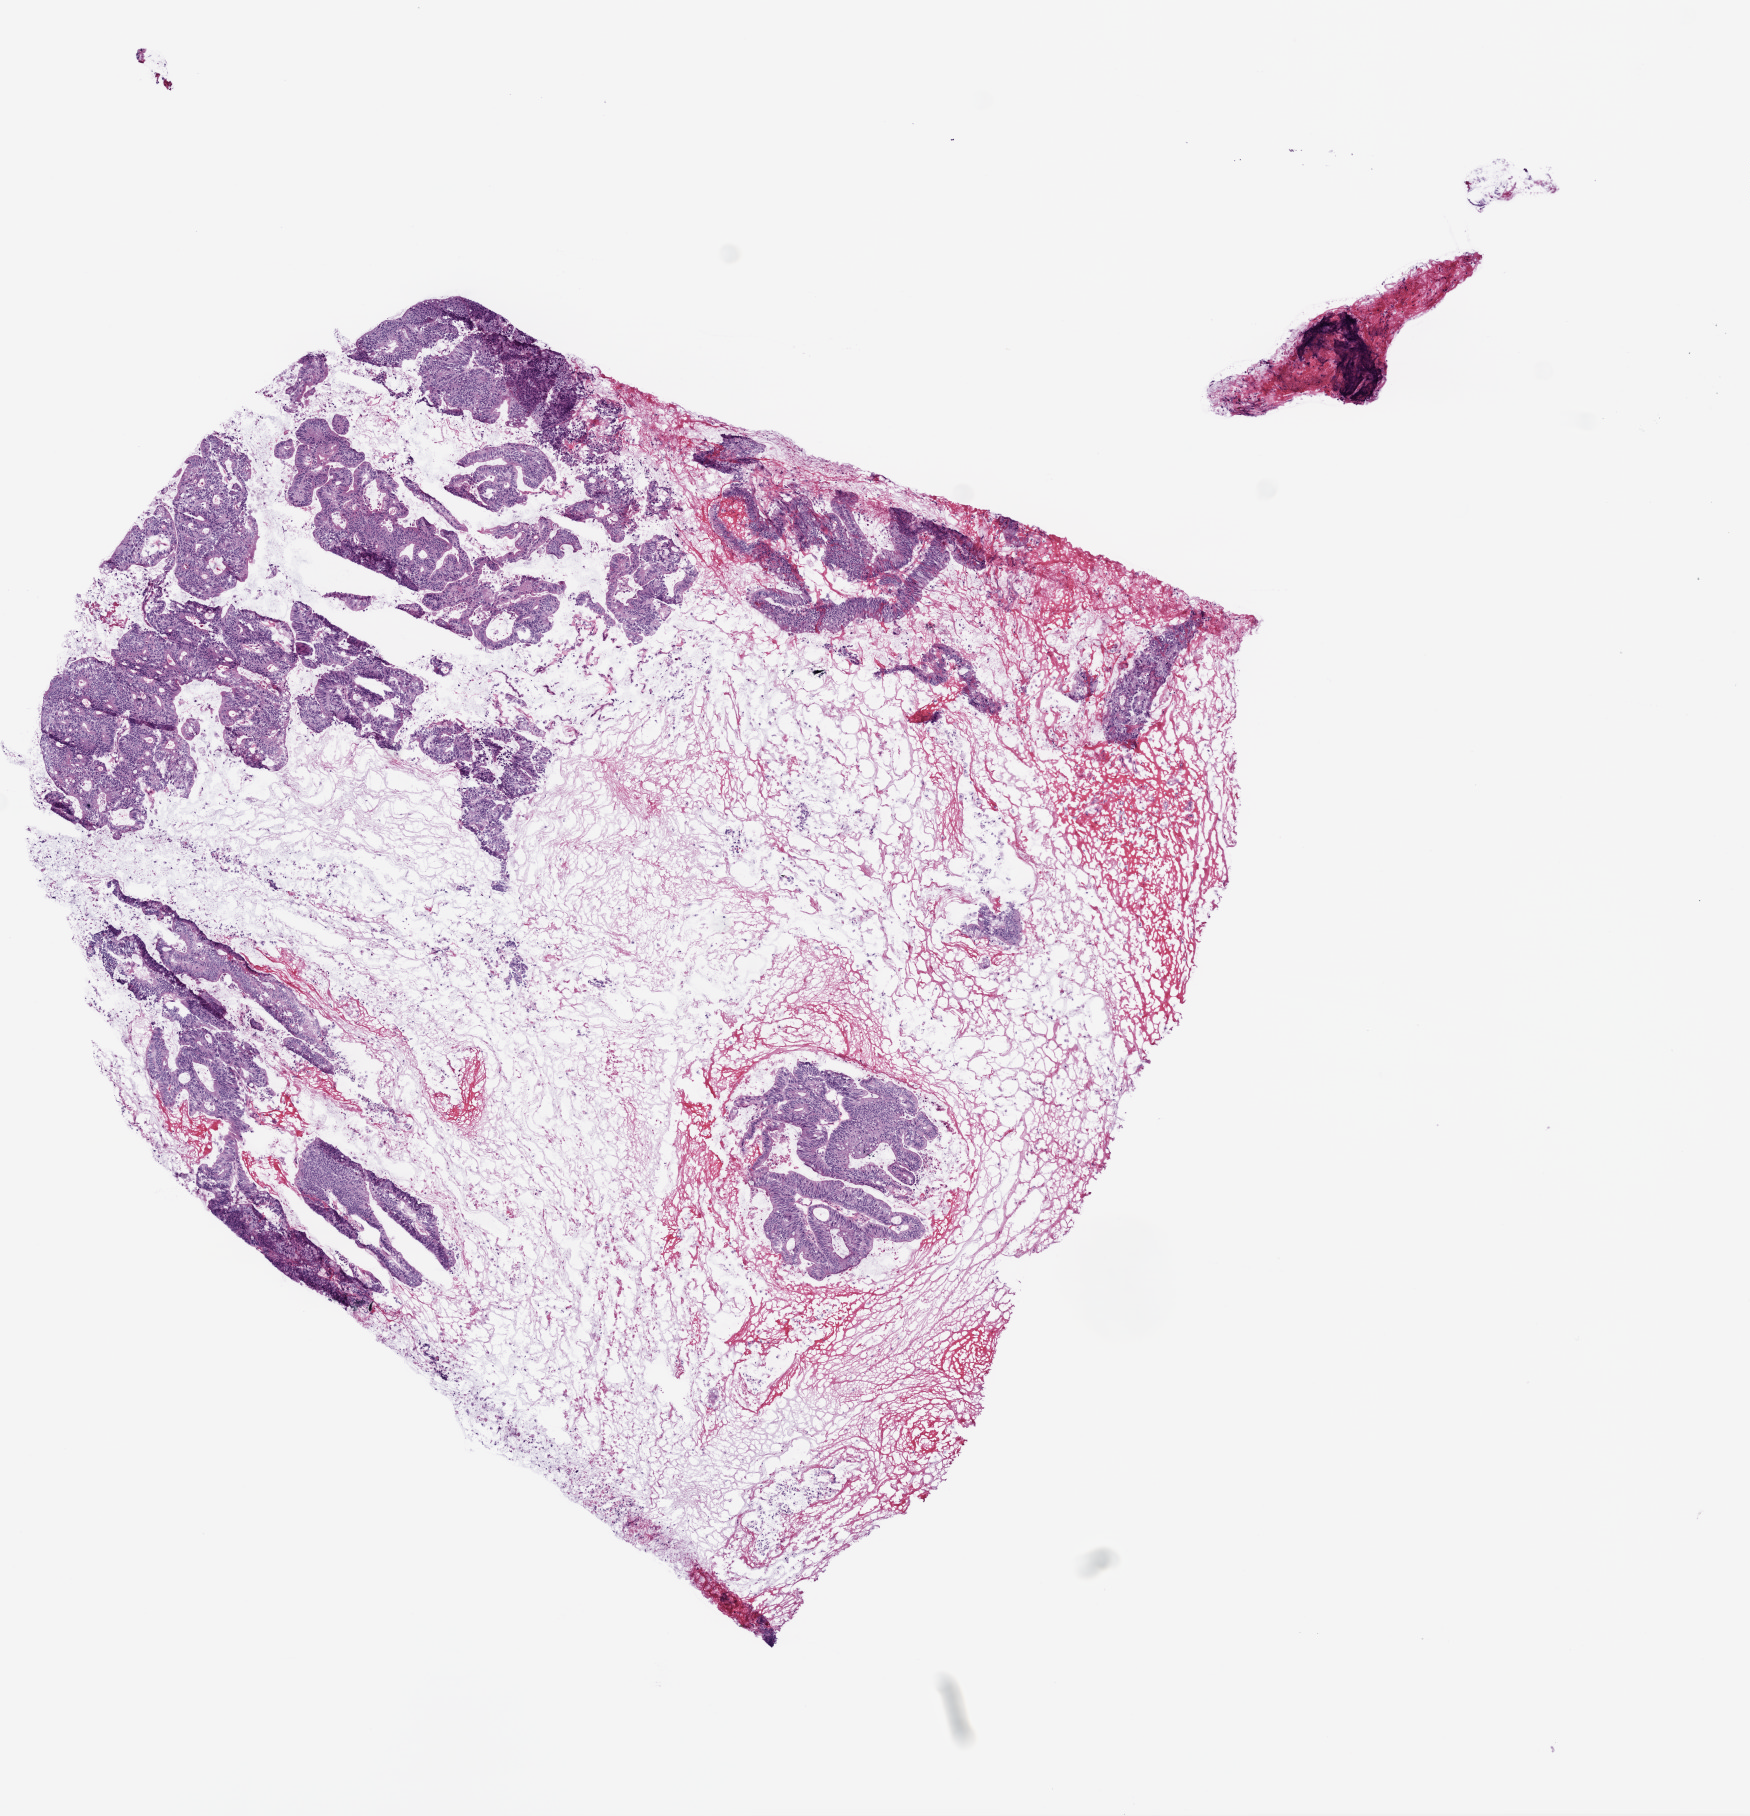
H&E whole-slide image — low-resolution overview of the scanned area, about 7.0 x 7.3 mm (slide scanned at 20x). Frozen section from the top of the tissue portion. Primary tumour sample from the colon. Male patient; age at initial diagnosis 70 years. Slide review estimates, as recorded: tumour cells 40%, tumour nuclei 80%, normal cells 0%, stromal cells 60%, necrosis 0%.
• lymph nodes positive (case pathology): 0 of 46 examined
• pathologic diagnosis: Adenocarcinoma, NOS (sigmoid colon)
• AJCC pathologic stage: I